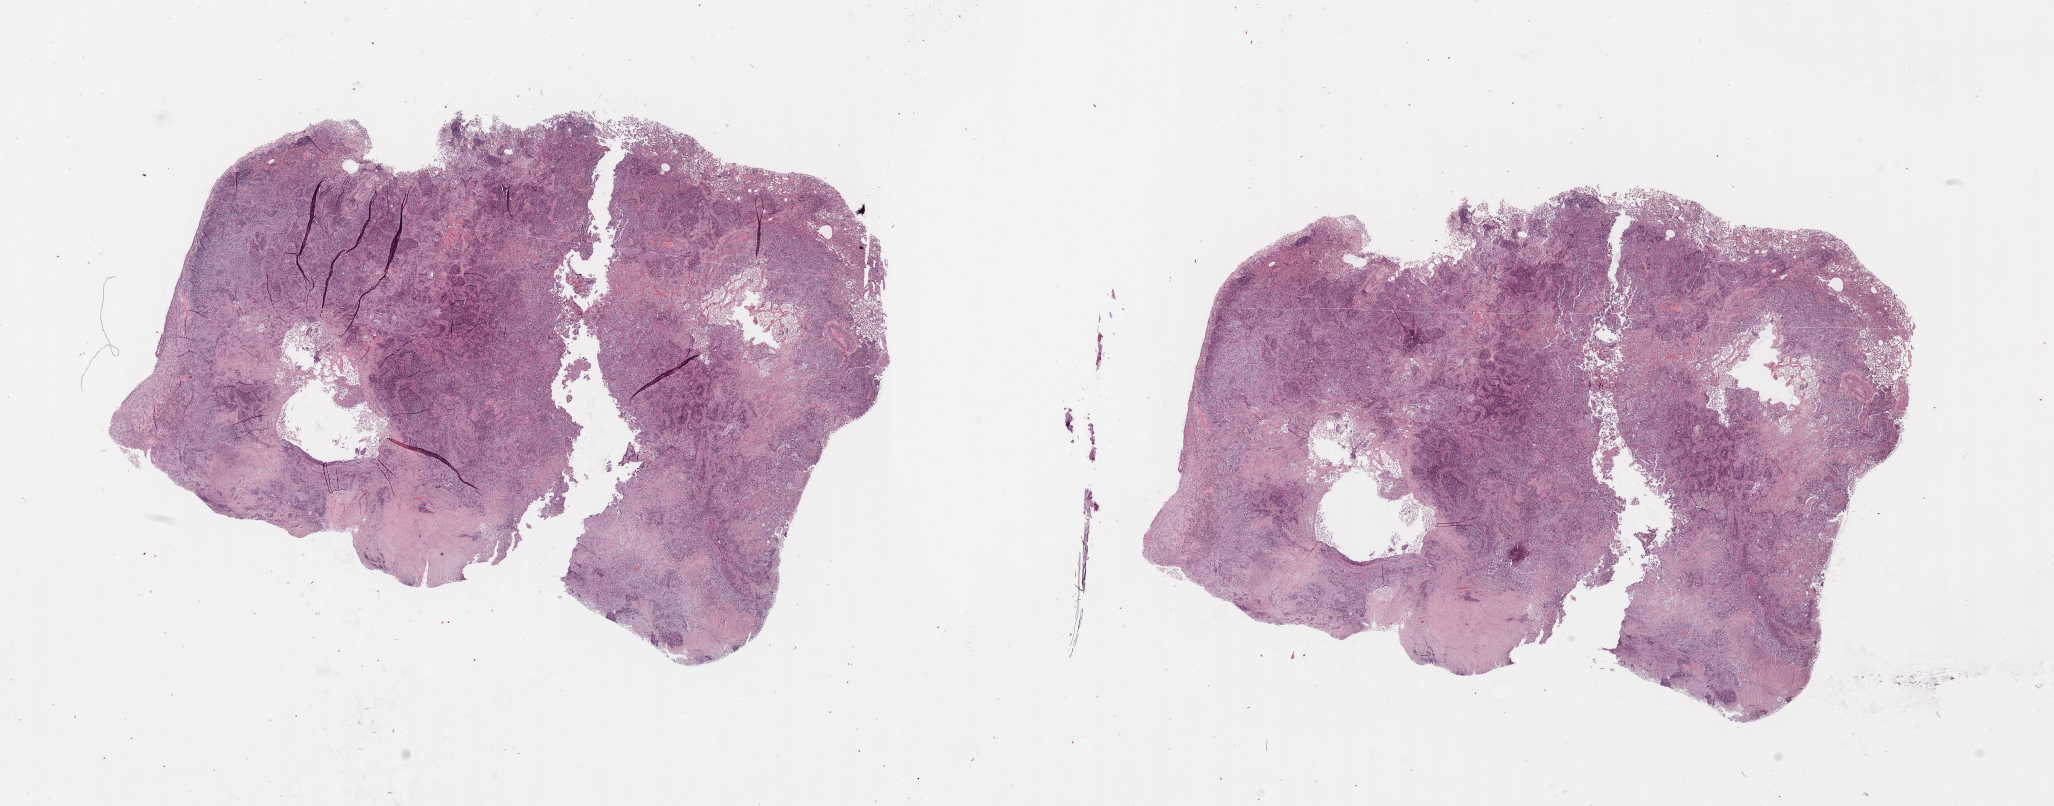
Whole-slide histology image, H&E — low-resolution overview of the scanned area, about 32.5 x 12.7 mm; lung, tumour tissue. Male, 57 y/o. Histologic grade: G3 (poorly differentiated).
Primary tumour site (as recorded): right lower lobe. Histologic diagnosis: Squamous cell carcinoma, NOS. AJCC pathologic stage: IA.